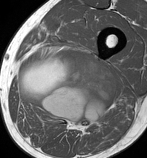
MRI of an extremity soft-tissue mass, one axial slice. Position 58 of 86 along the scan axis. MR volume resampled by the dataset authors to the PET/CT grid (not the native acquisition matrix). 147 × 158 image matrix. Male patient. Case-level facts recorded for this patient, not image findings: histological type: undifferentiated pleomorphic liposarcoma; grade: high; site of the primary tumour: left thigh.
Annotated regions visible in this slice (expert contour drawn on MRI and transferred to this co-registered scan by the dataset authors):
- gross tumour volume including surrounding oedema: bounding box [x1, y1, x2, y2] px = [18, 51, 118, 130]
- gross tumour volume (mass): [18, 51, 118, 127]